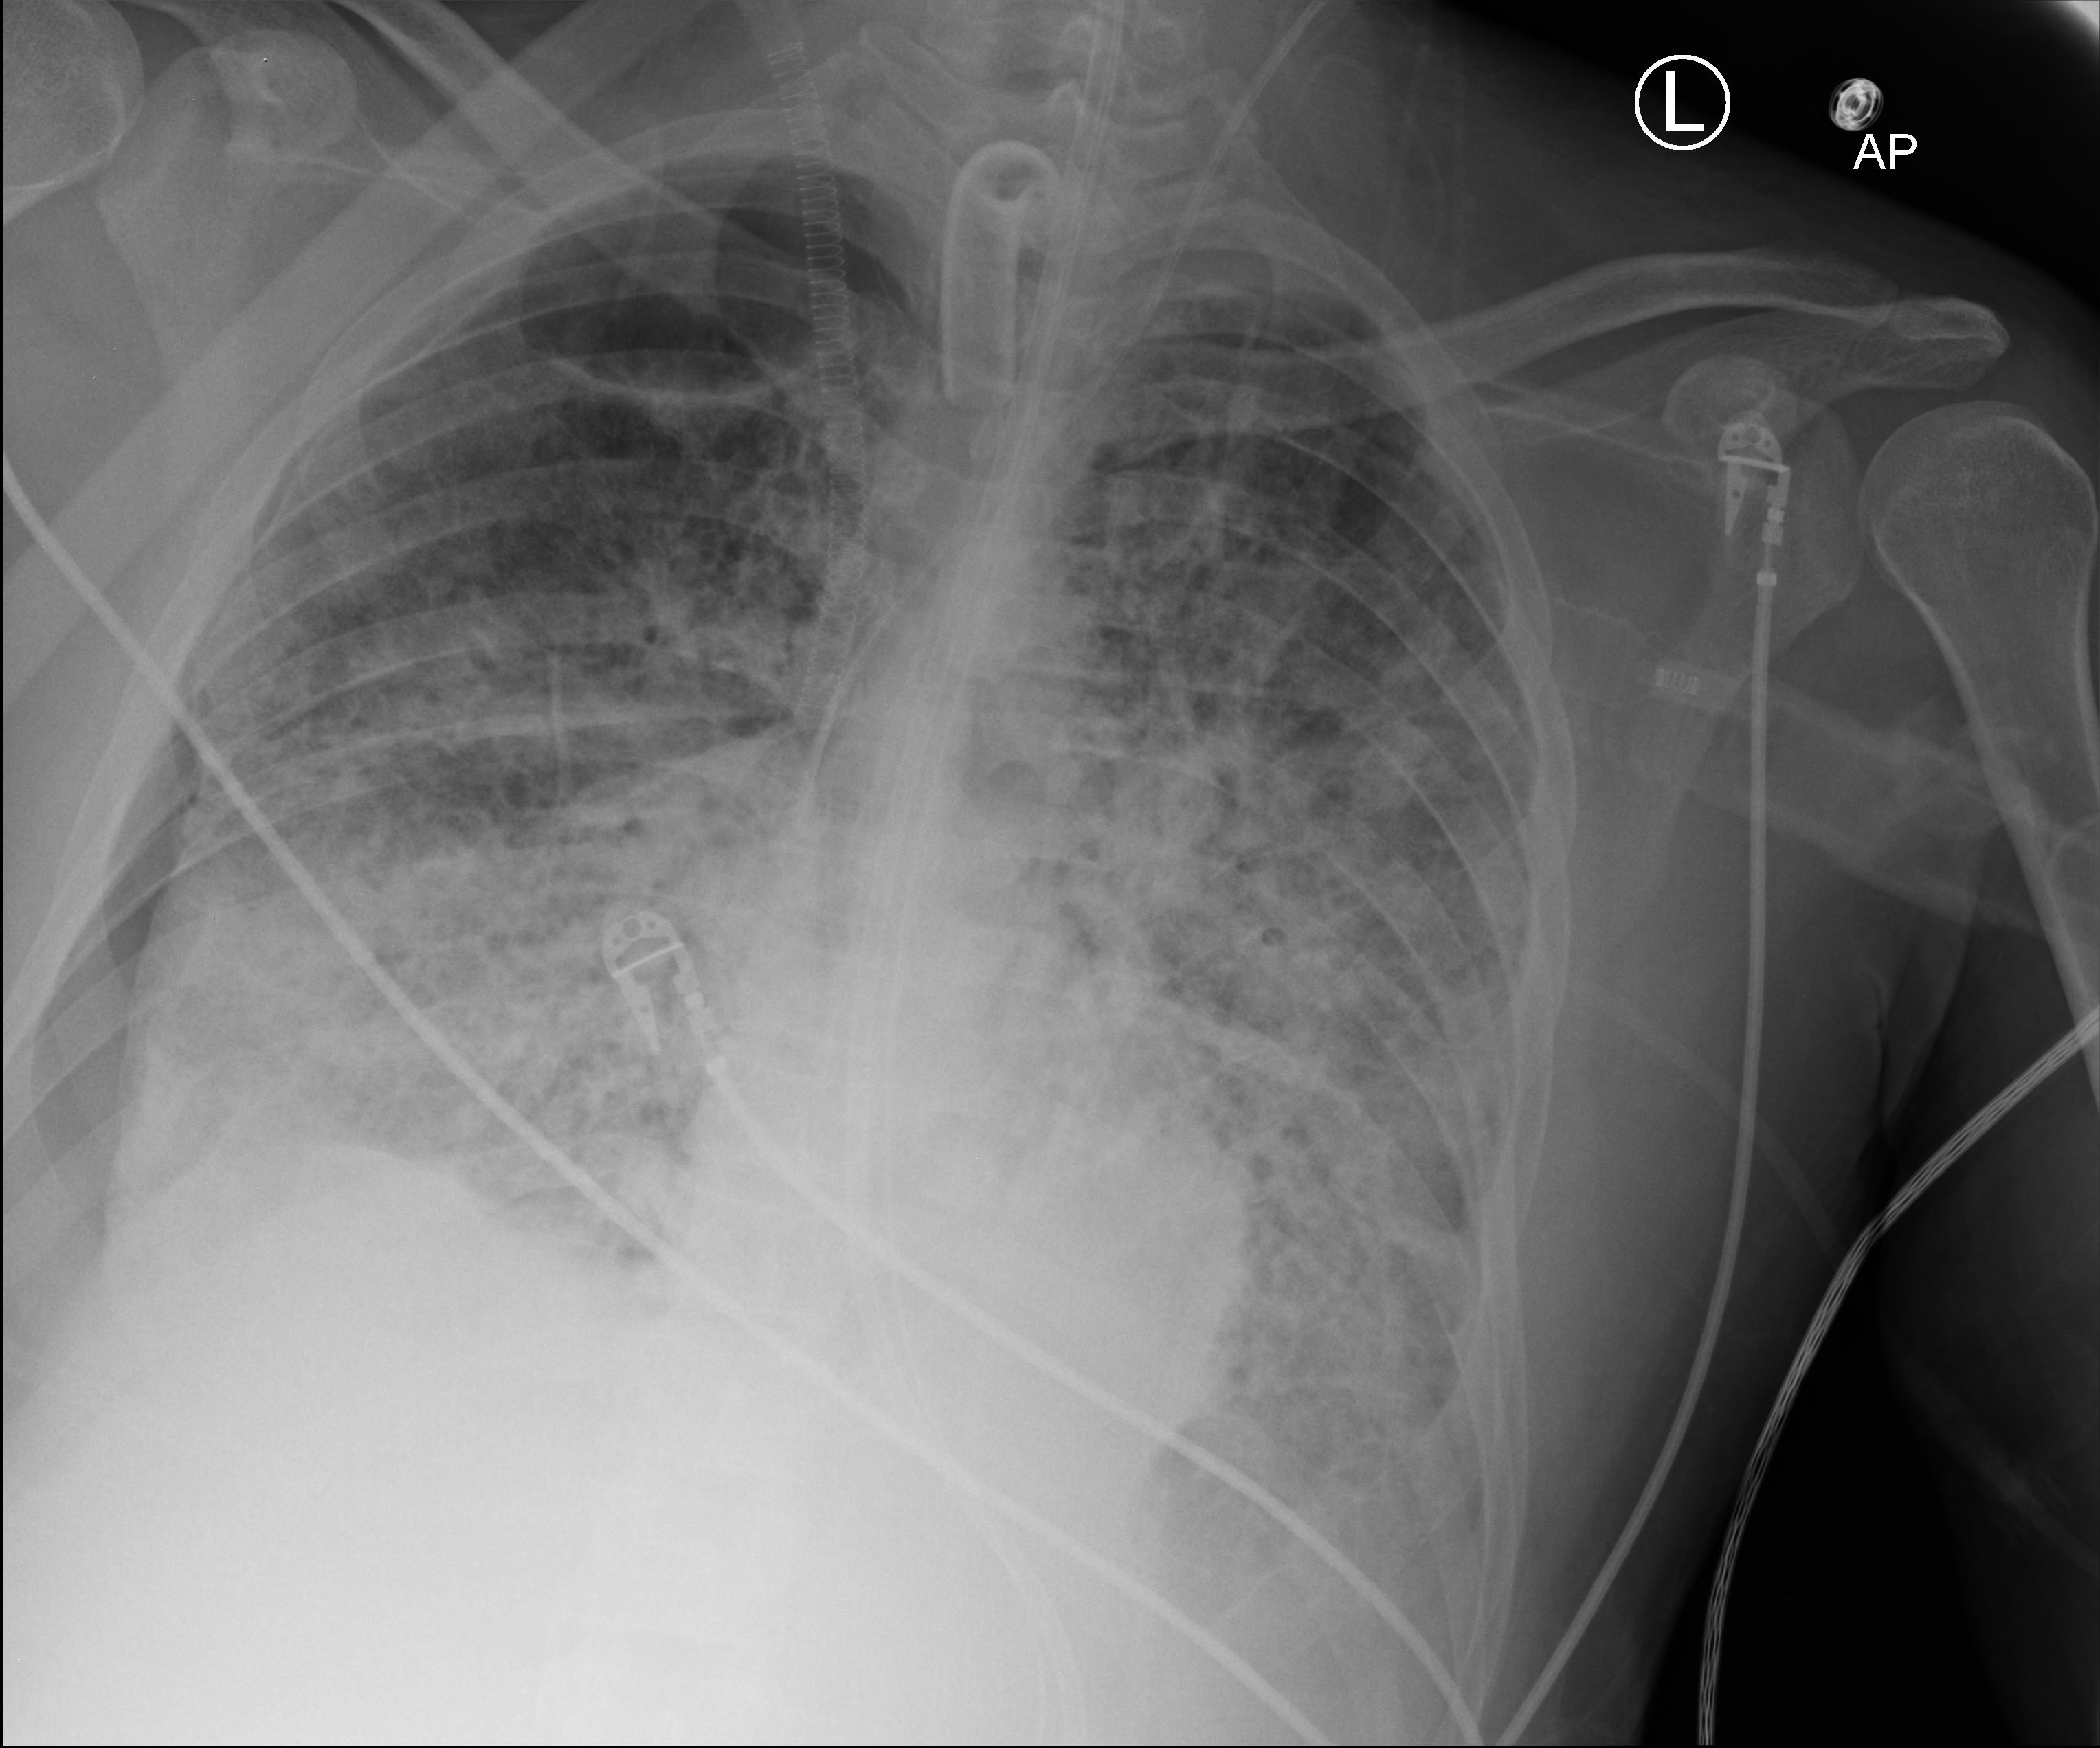
Bedside chest radiograph (computed radiography), anteroposterior (AP) projection. Adult patient hospitalised with COVID-19, age 18–59 years.
Hospital-stay facts (about this admission, not read from this image; timing relative to this image not recorded): mechanically ventilated during this hospital stay: yes.